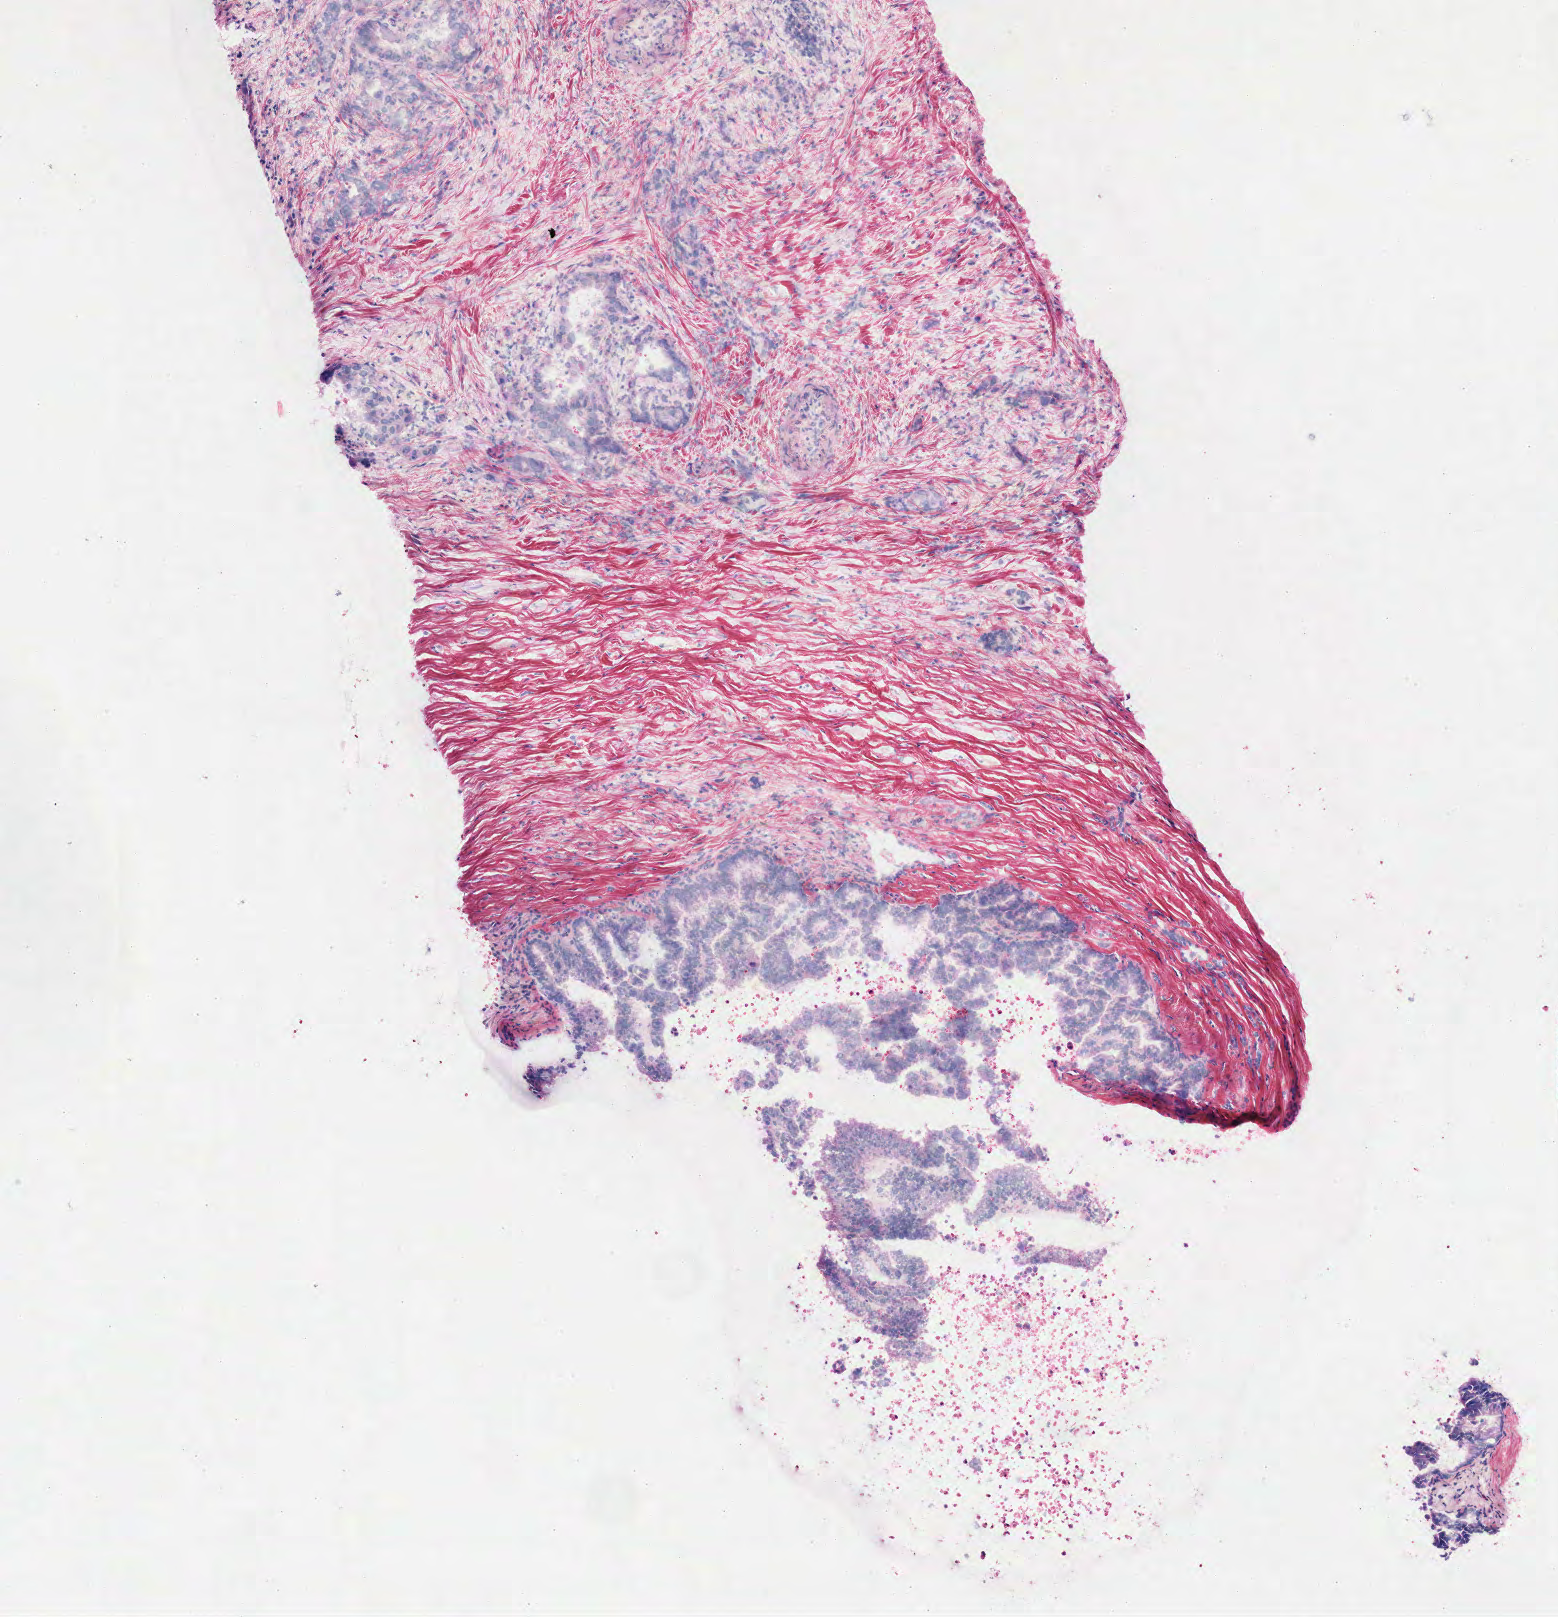
H&E whole-slide image, shown as a low-resolution overview of the whole scanned area (about 3.1 x 3.3 mm, slide scanned at 40x). Frozen section from the top of the tissue portion. Pancreas, primary tumour sample. Male, age 41 years at initial diagnosis. Histologic grade: G2 (moderately differentiated). Pathologist review of this section (percent, as recorded): tumour cells 95%, tumour nuclei 85%, normal cells 0%, stromal cells 5%, necrosis 0%. Inflammatory infiltration, as recorded: lymphocyte infiltration 0%, monocyte infiltration 0%, neutrophil infiltration 0%.
• pathologic diagnosis: Infiltrating duct carcinoma, NOS
• AJCC pathologic stage: IIB